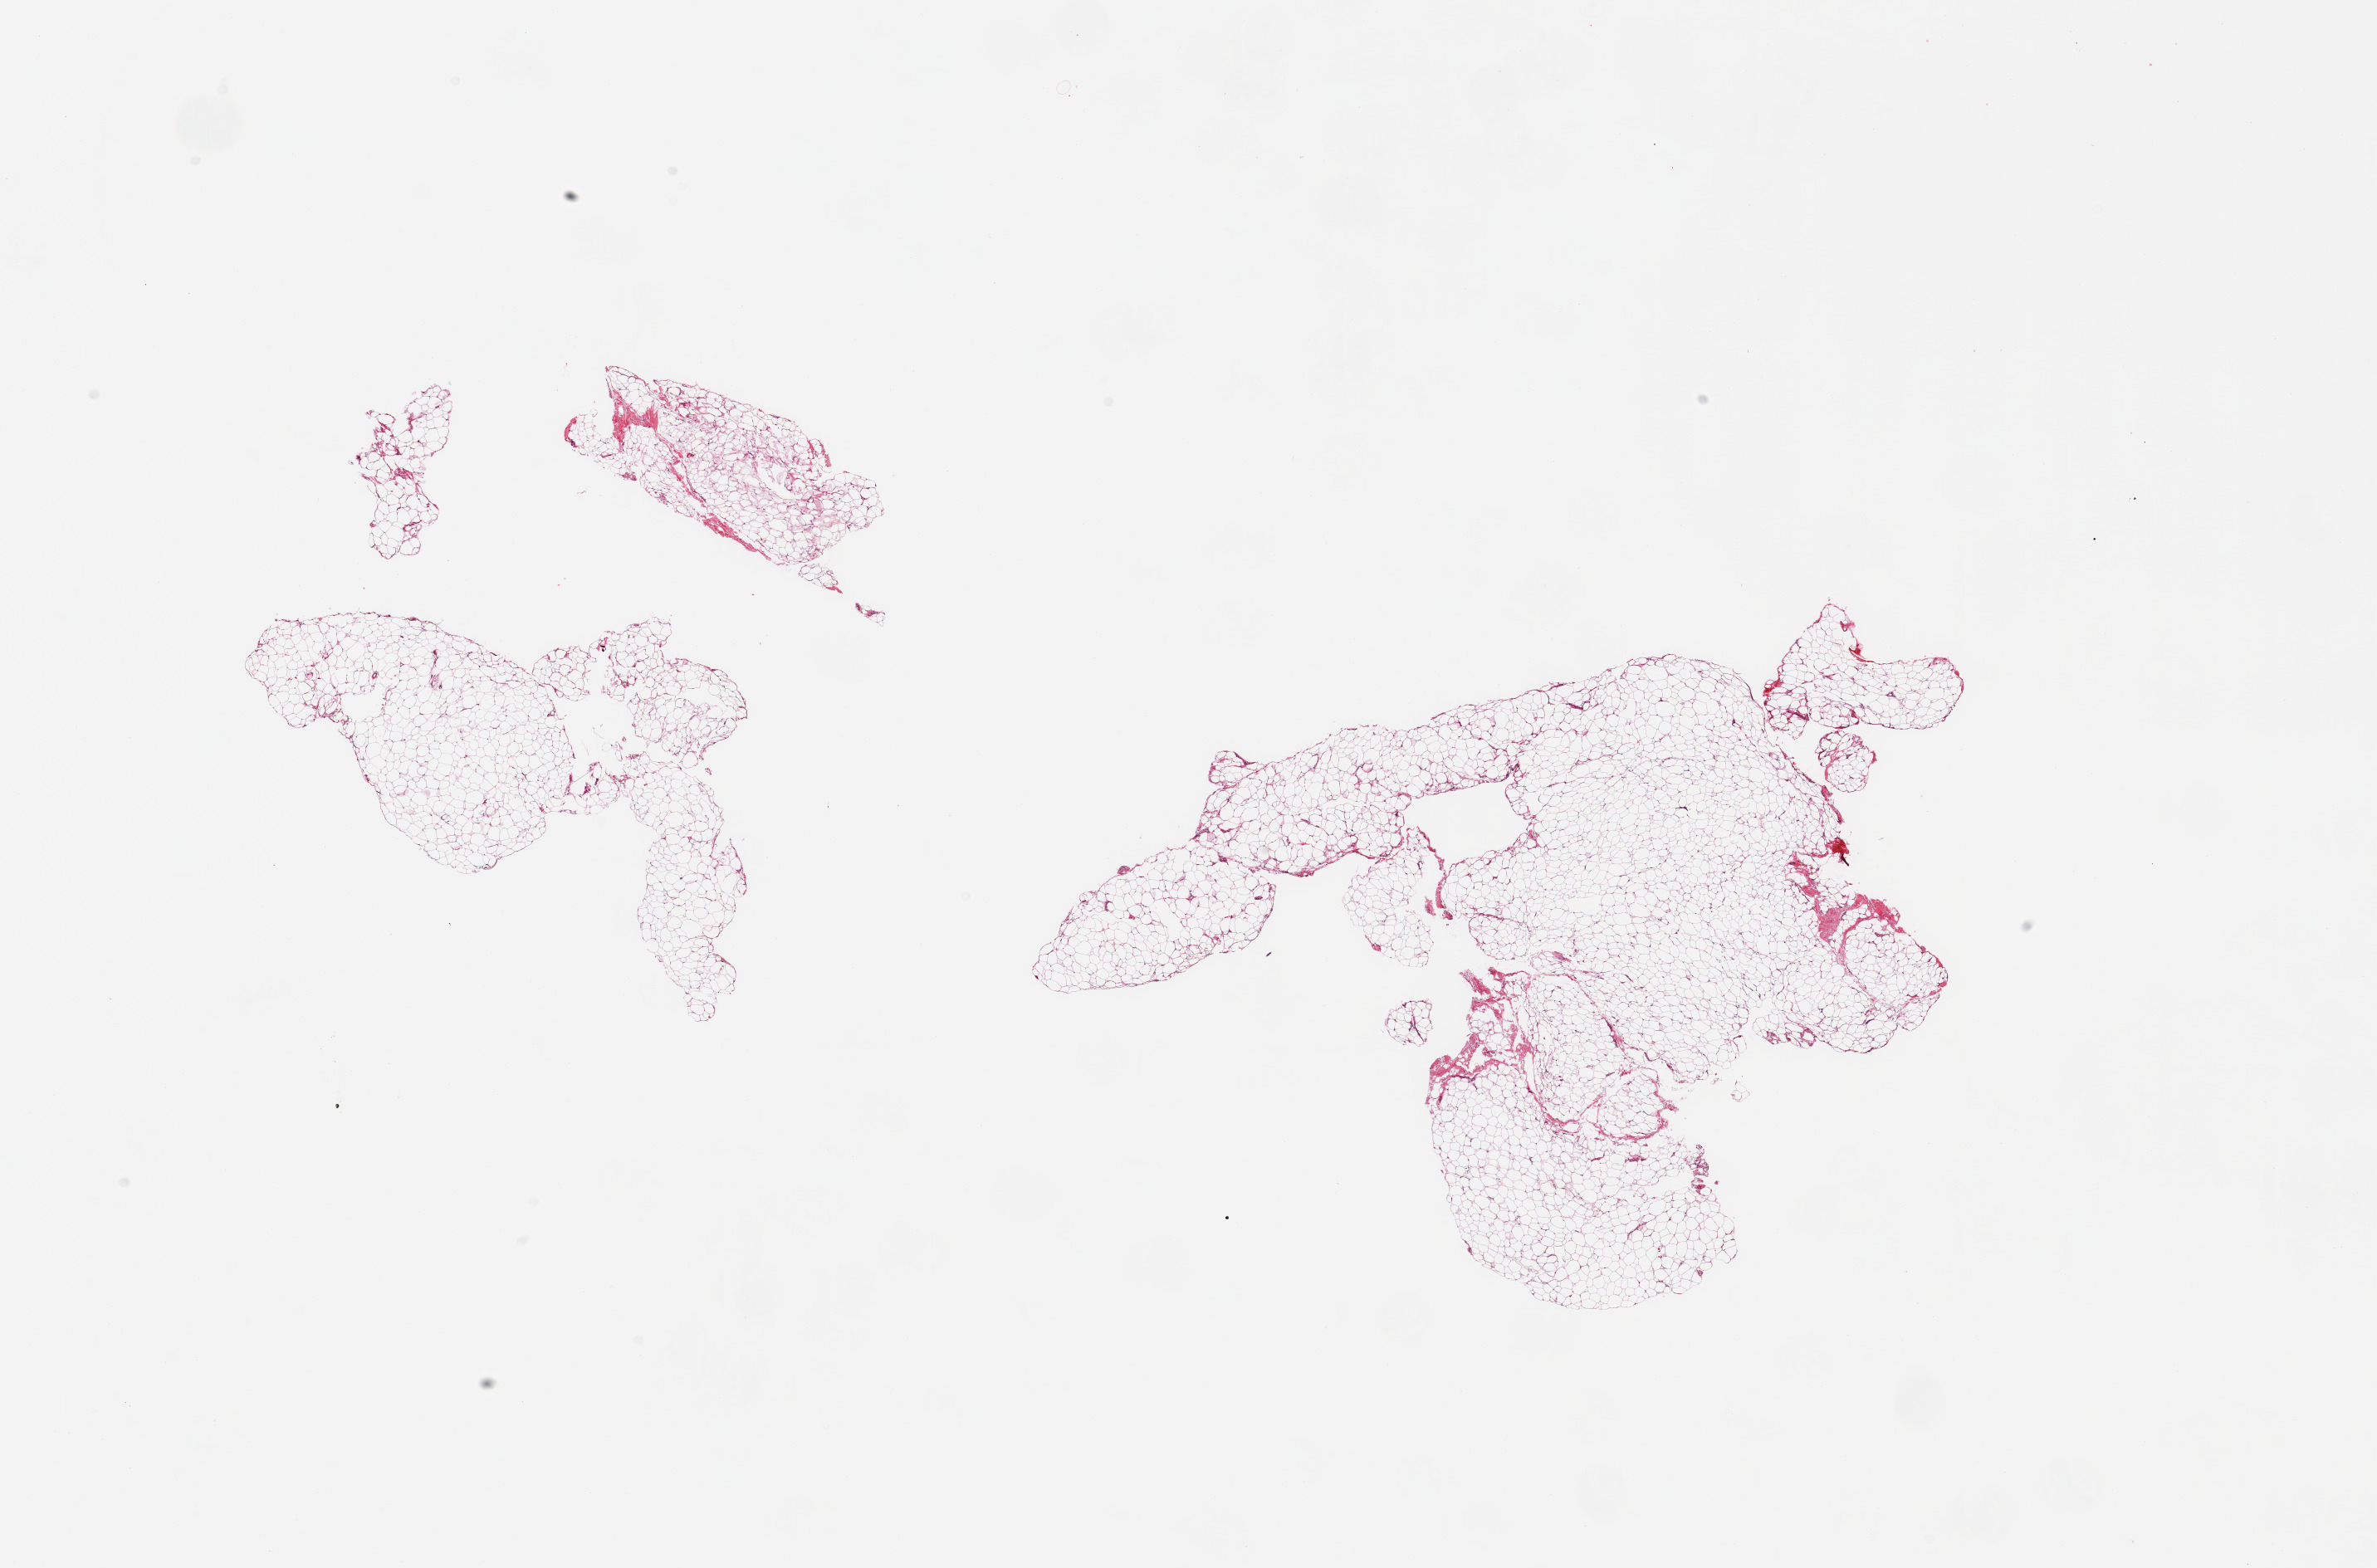
Digitized haematoxylin and eosin-stained section — low-resolution overview of the scanned area, about 22.6 x 14.9 mm (acquisition: 20x scan), PAXgene-fixed, paraffin-embedded tissue, target tissue: adipose tissue, tissue donor sample. Male donor.
- review note (as recorded): 2 pieces, trace fascia <5% tissue